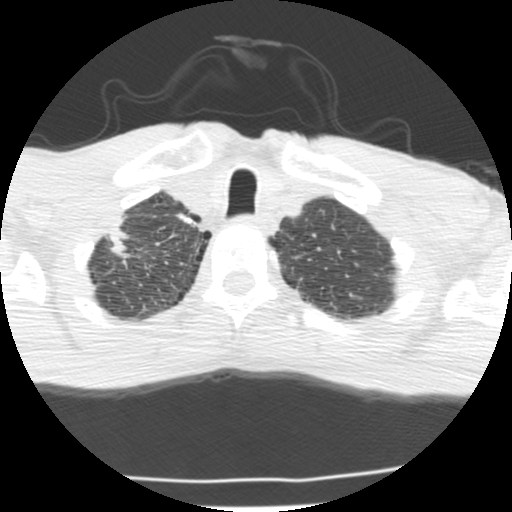
Low-dose screening chest CT, one axial slice; position 189 of 214 along the scan axis; lung window (W 1500 / L -600 HU); 2.5 mm slice thickness; 512 × 512 image matrix, field of view 283 × 283 mm.
Annotated regions visible in this slice (expert manual segmentation):
- lesion 1 (tumor, upper lobe of right lung): box from (x=107, y=218) to (x=130, y=264) px